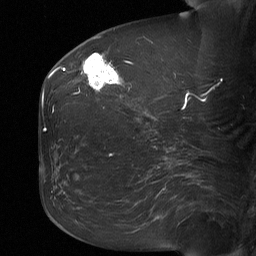
Breast MRI (dynamic contrast-enhanced), one sagittal slice; slice 25 of 64 in the series (ordered by position); dynamic contrast-enhanced study with each time point stored as its own series, time point 2 of 3 at this slice position (early post-contrast, ordered by acquisition time); 1.5 T; TE 4.8 ms, TR 27 ms; 2 mm slice thickness; 256 × 256 image matrix. Patient: female, 60 years. From the clinical record (not read from this slice): setting: breast cancer imaged before/during neoadjuvant chemotherapy; receptor status: HR-positive, HER2-negative.
Annotated regions visible in this slice (semi-automatic segmentation, software-assisted and operator-edited):
- analysis volume of interest (the breast-tissue region the enhancement analysis was run in; not a lesion): bounding box (x1, y1, x2, y2) in pixels: (79, 53, 122, 95)
- tumour enhancement mask (voxels above the 90 % enhancement threshold inside the analysis volume of interest): (83, 53, 118, 90)